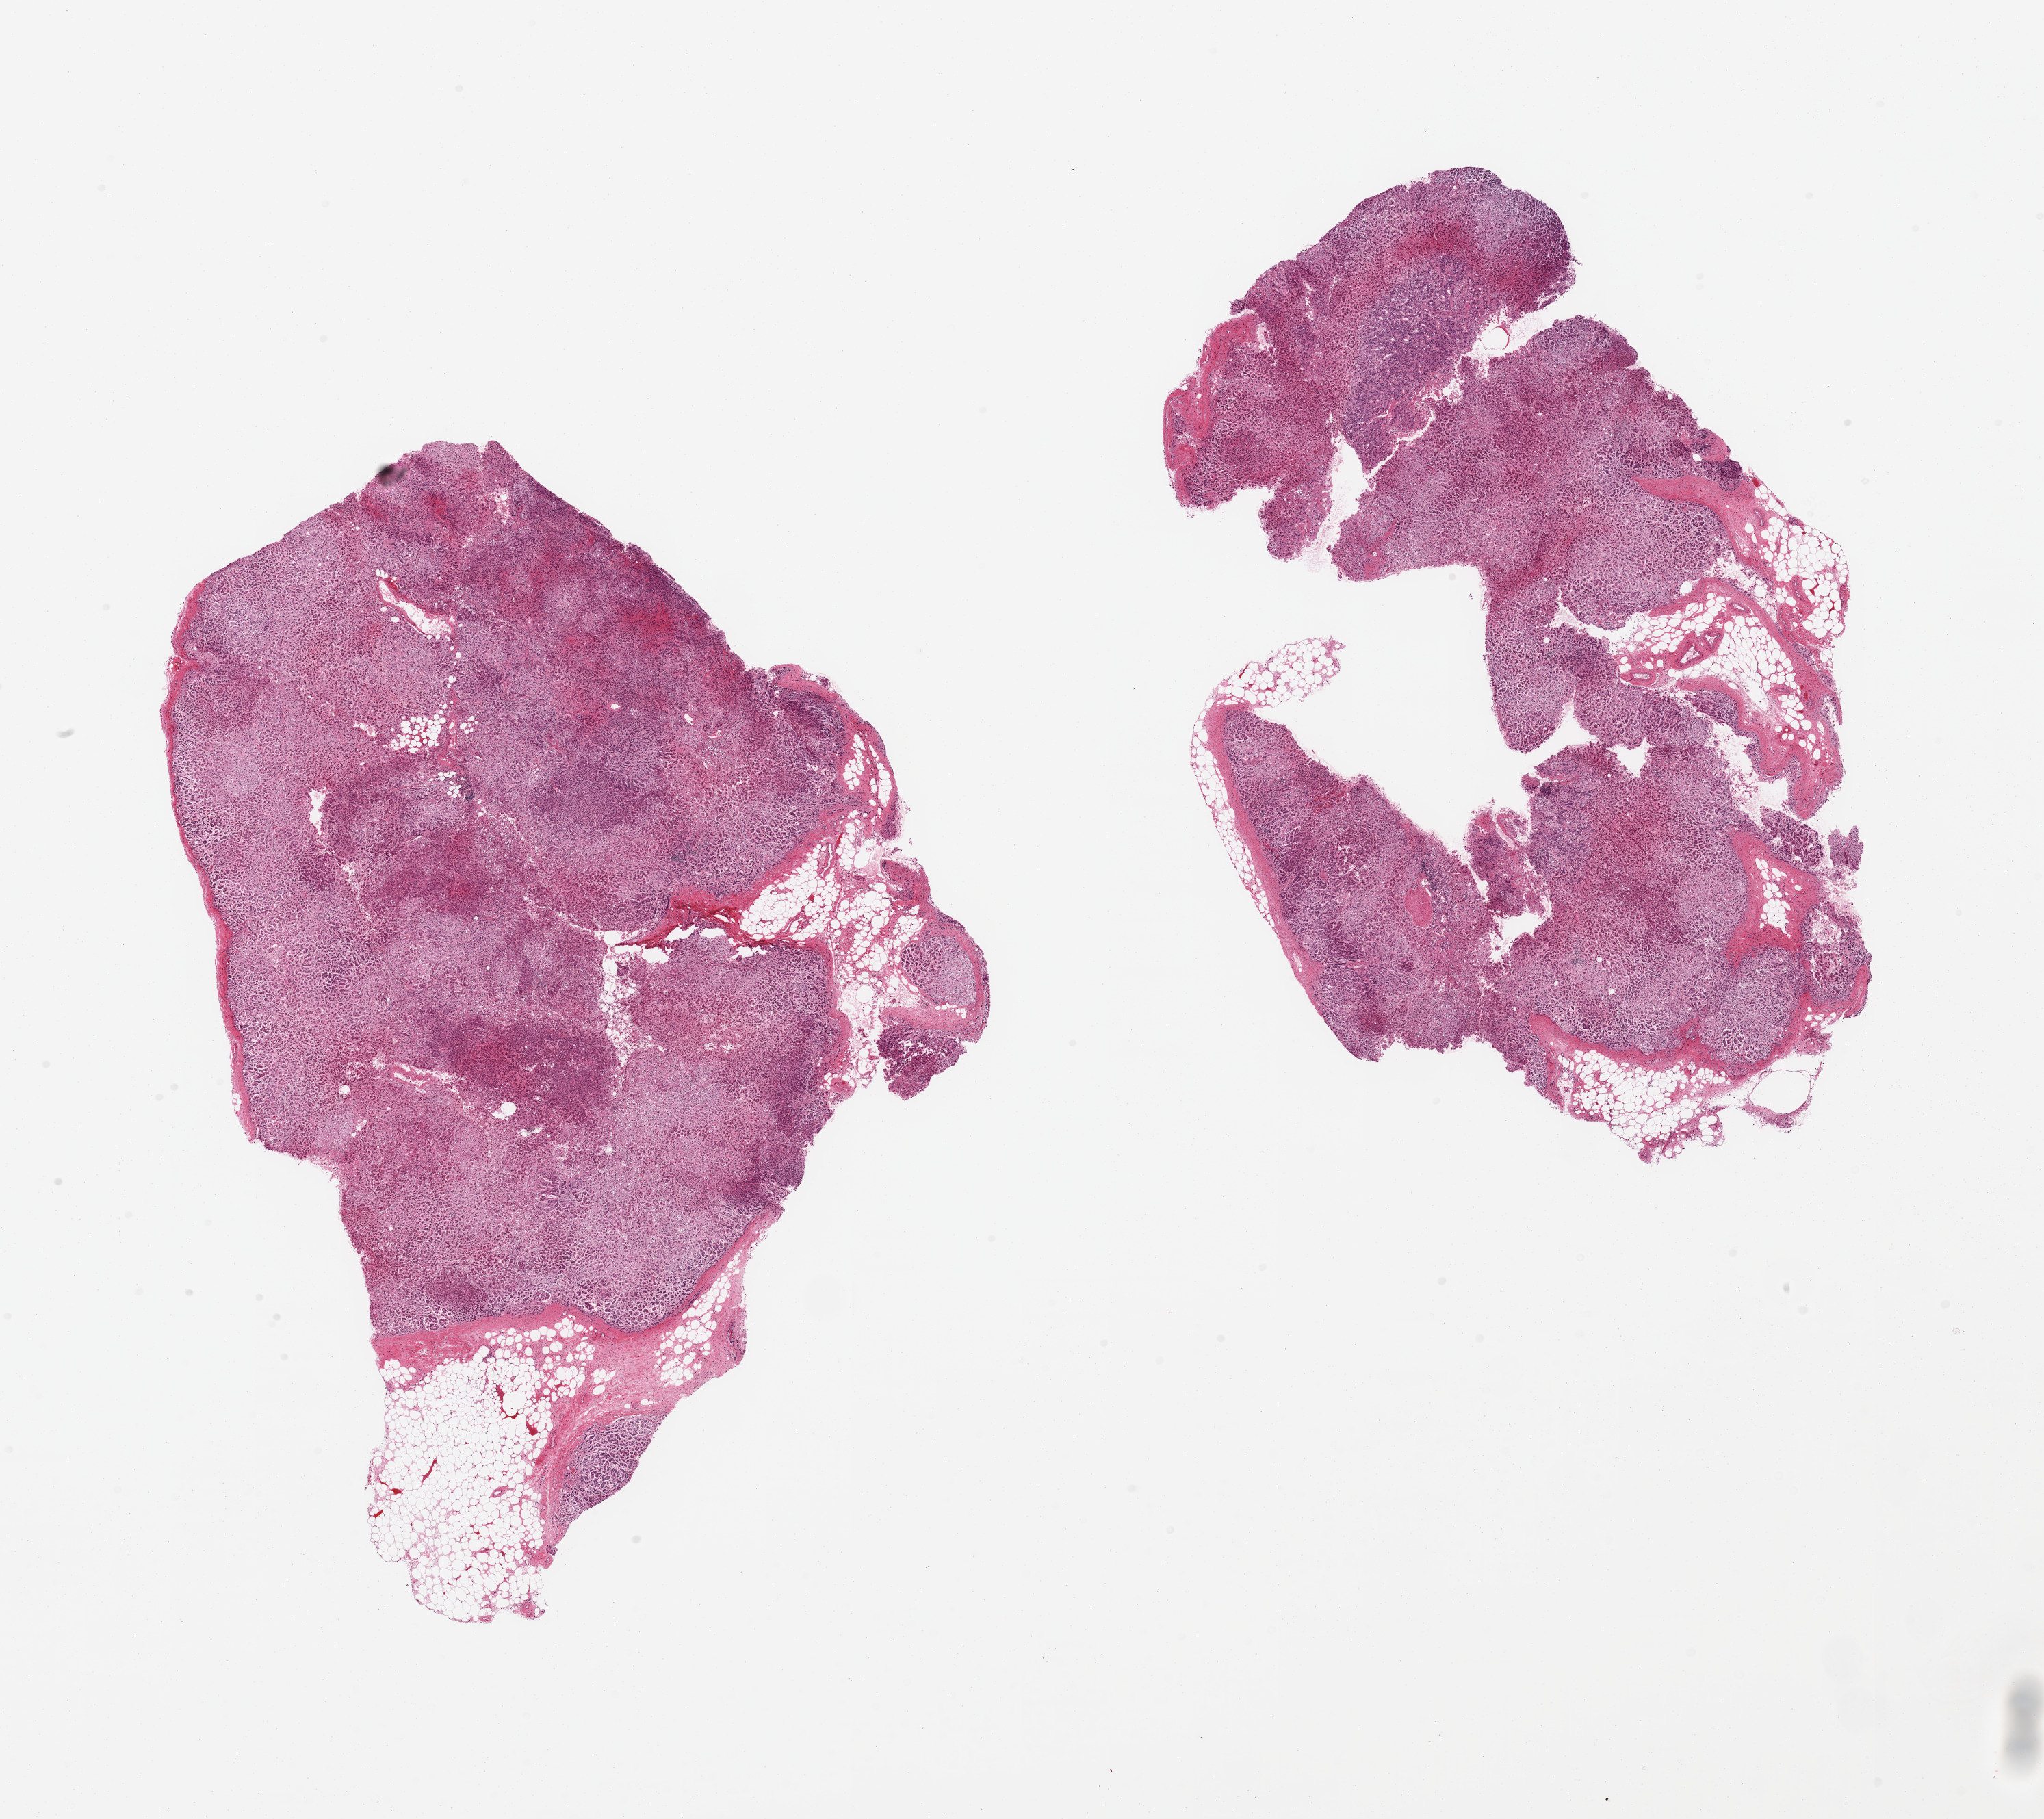
Whole-slide image, H&E stain — a low-resolution overview of the entire scanned area, about 23.6 x 21.0 mm (acquisition: 20x scan), PAXgene-fixed, paraffin-embedded tissue, target tissue: adrenal gland, tissue donor sample. Donor sex: male.
Pathologist's review note for this sample: 2 pieces, cortex; adherent fat up to ~10% of tissue.